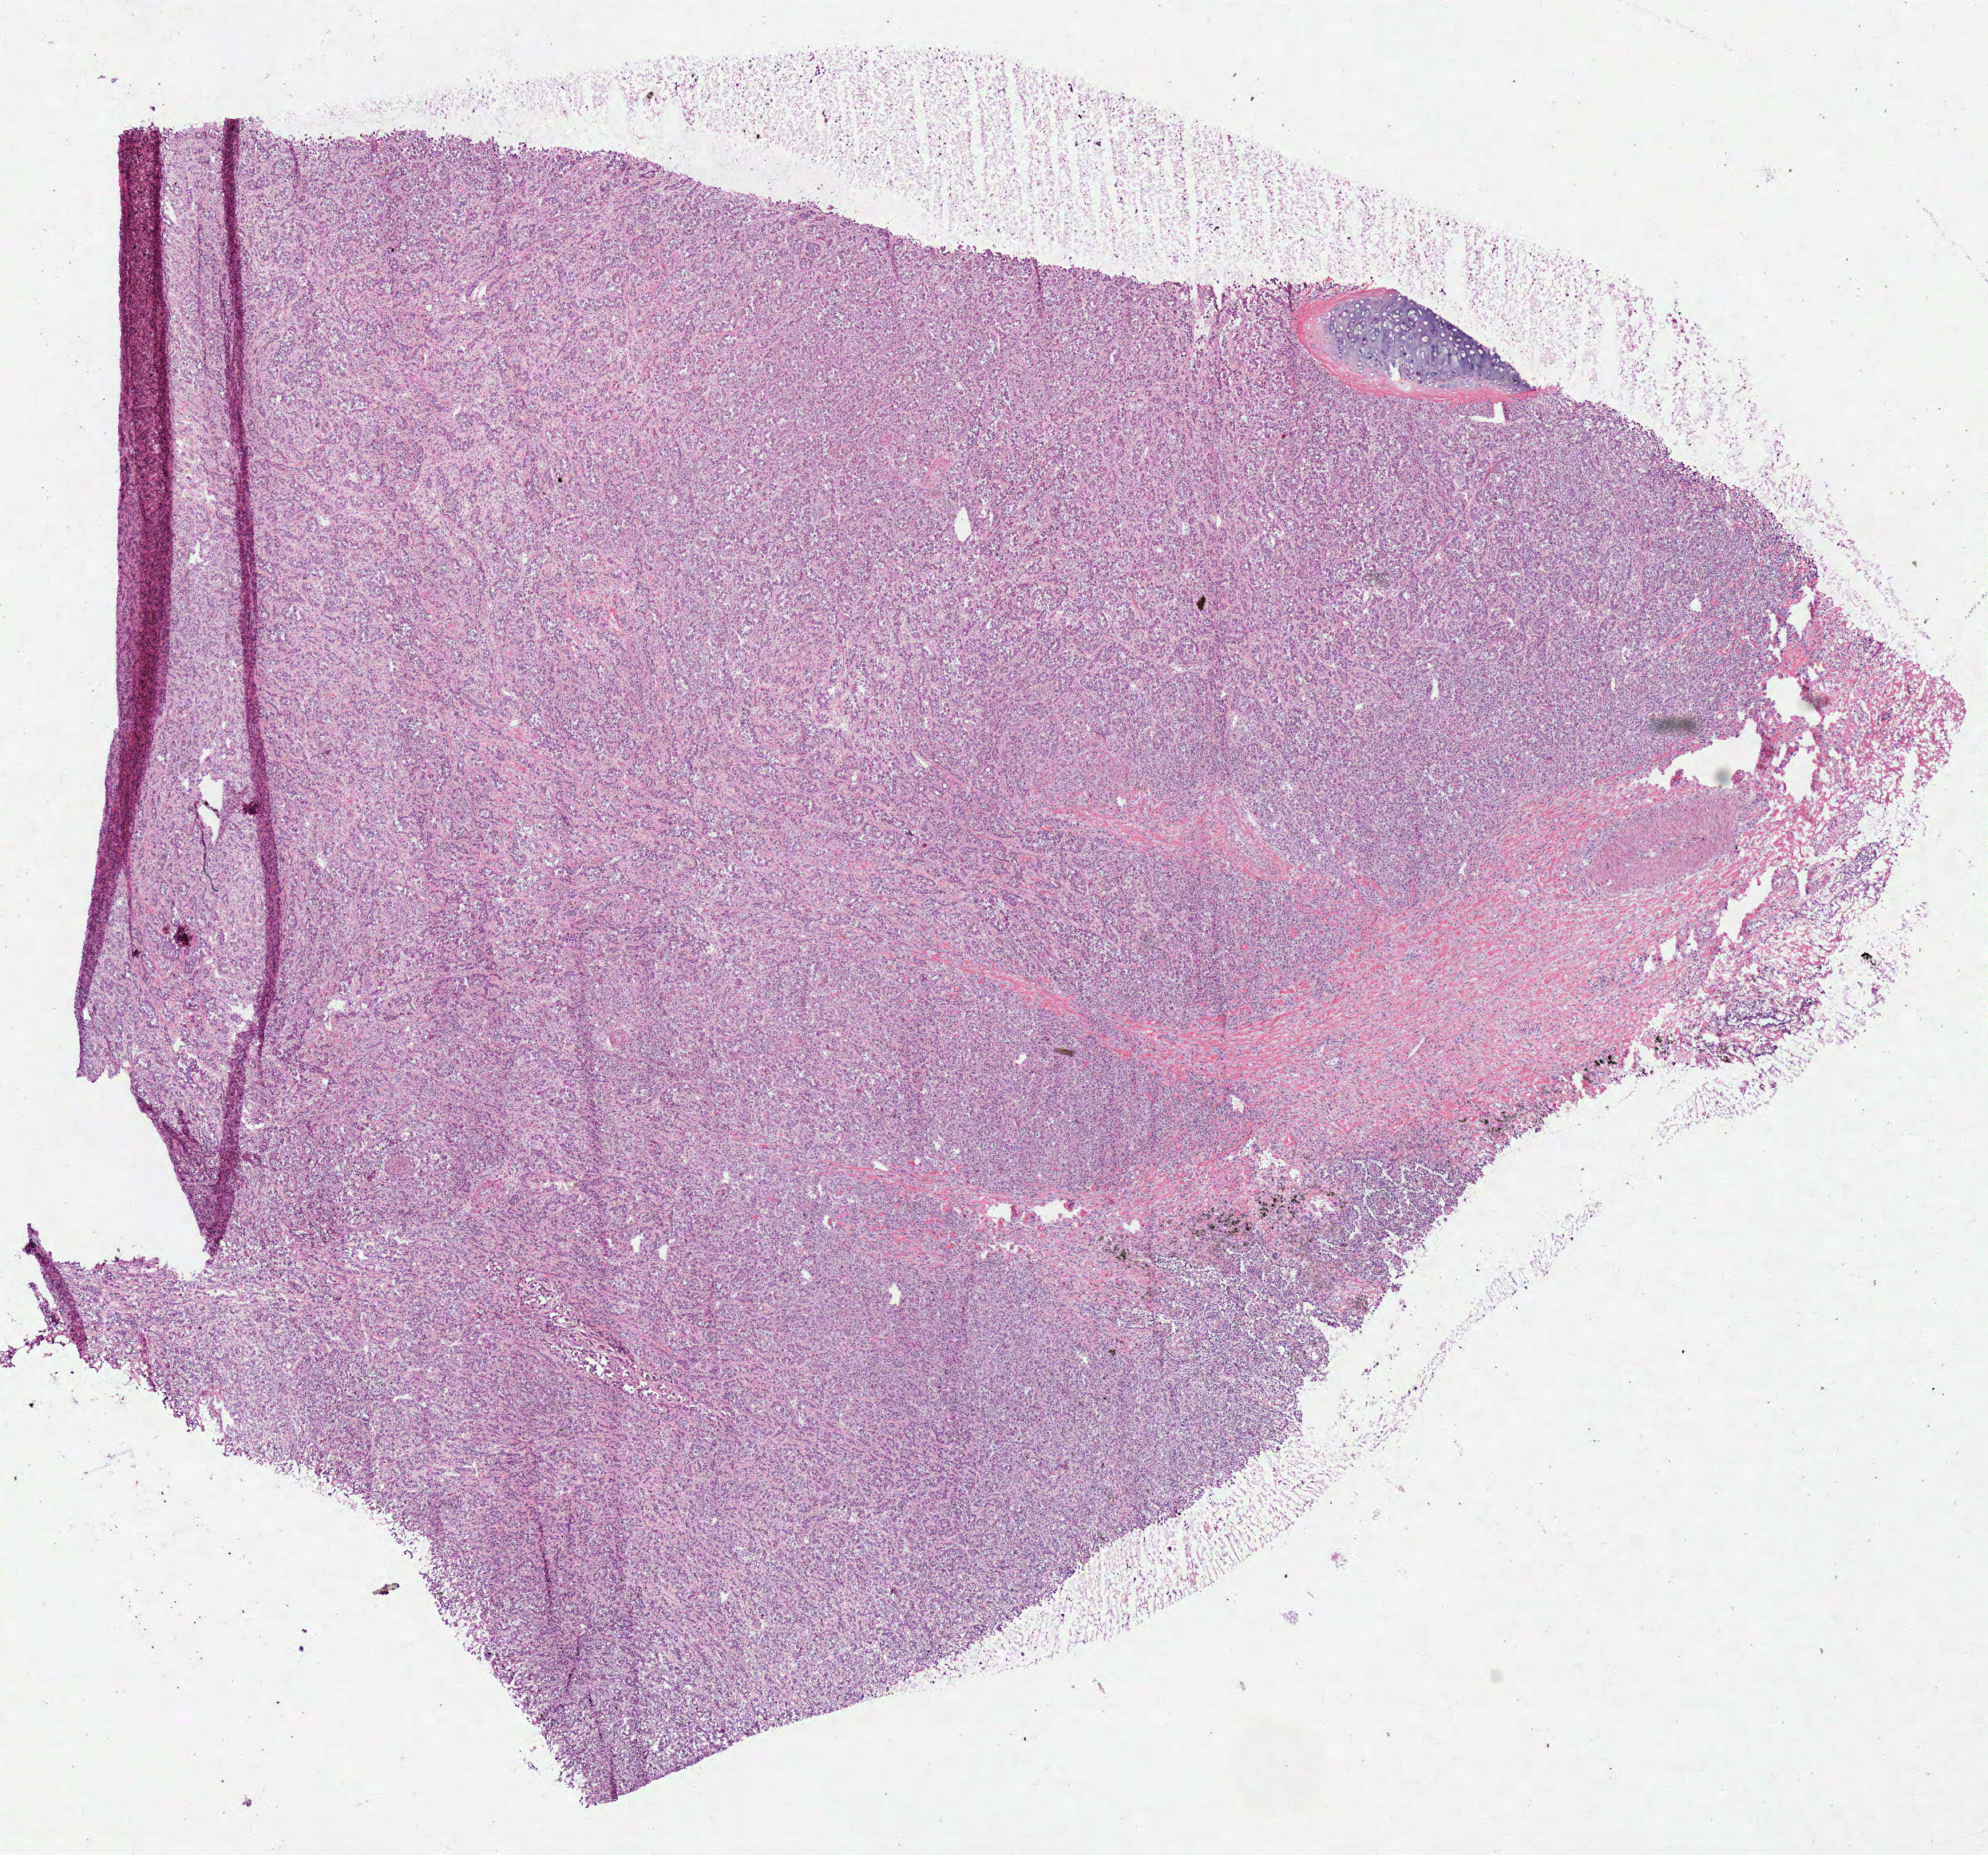
Digitized Hematoxylin and eosin (H&E) stained tissue section (whole slide), a low-resolution overview of the entire scanned area, about 9.8 x 9.1 mm, frozen section from the bottom of the tissue portion, lung, primary tumour sample. Female, age 50 years at initial diagnosis. Slide review estimates, as recorded: tumour cells 93%, tumour nuclei 85%.
Pathologic diagnosis: Adenocarcinoma, NOS.